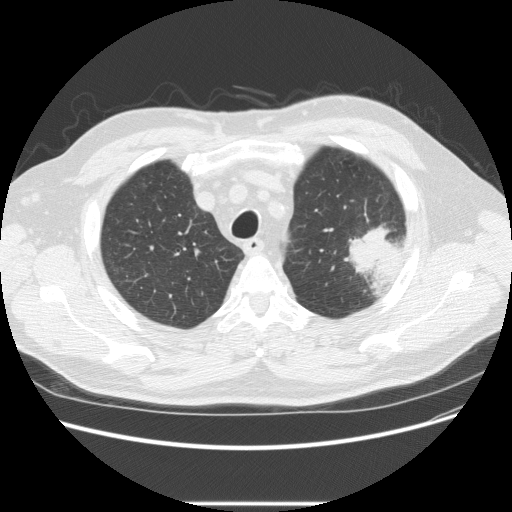
Chest CT (low-dose screening protocol), one axial image; baseline screening round; lung window (W 1500 / L -600 HU); 2.5 mm slice thickness; slice 50 of 233 in the series; 512 × 512 image matrix, field of view 380 × 380 mm. Male, age 73 years at enrolment.
- Expert-annotated lung lesion, bounding box (x1, y1, x2, y2) in pixels: (332, 216, 411, 285).
- The screening reader recorded 2 non-calcified nodules or masses ≥4 mm on this exam (left upper lobe, right upper lobe); which of them this box marks is not recorded.
- Later outcome: lung cancer diagnosed 11 days after this screen — bronchiolo-alveolar adenocarcinoma, NOS, other location, well differentiated (G1), stage IV (AJCC 6th edition).